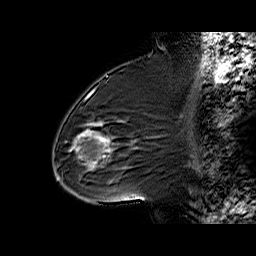
Breast MRI (dynamic contrast-enhanced), one sagittal slice. Position 35 of 60 along the scan axis. Dynamic contrast-enhanced series, time point 2 of 6 at this slice position (early post-contrast). 1.5 T. TE 6.3 ms, TR 32.4 ms. 4 mm slice thickness. 256 × 256 image matrix. Female patient. Case-level facts recorded for this patient, not image findings: setting: breast cancer imaged before/during neoadjuvant chemotherapy; receptor status: triple-negative.
Annotated regions visible in this slice (semi-automatically segmented with operator editing):
- analysis volume of interest (the breast-tissue region the enhancement analysis was run in; not a lesion): bounding box (x1, y1, x2, y2) in pixels: (65, 88, 146, 187)
- tumour enhancement mask (voxels above the 100 % enhancement threshold inside the analysis volume of interest): (75, 123, 112, 165)